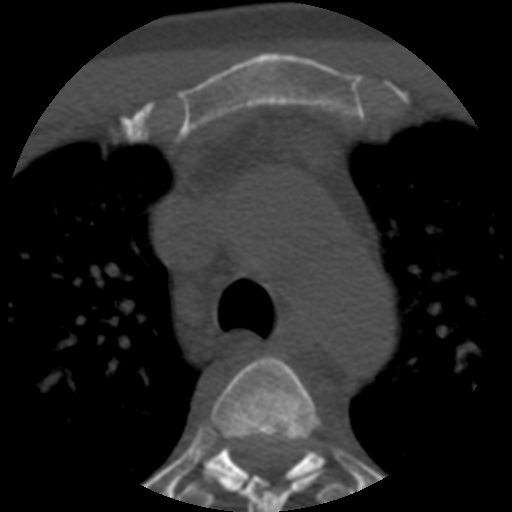
CT including the spine, one axial slice; position 406 of 508 along the scan axis; reconstruction kernel STANDARD; 120 kVp; bone window (W 1800 / L 400 HU); 512 × 512 image matrix, field of view 160 × 160 mm. Patient age 57 years. From the clinical record (not read from this slice): primary cancer: prostate.
Structures marked on this image (semi-automatically segmented with operator editing):
- T3 vertebra: bounding box [x1, y1, x2, y2] px = [205, 356, 319, 512]
- T4 vertebra: [175, 434, 359, 507]